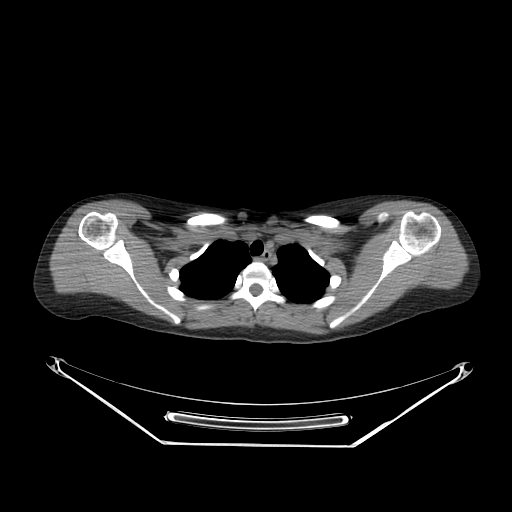
CT of an extremity soft-tissue mass (from a PET/CT study), one axial slice. Slice 213 of 267 in the series (ordered by position). 140 kVp. Soft-tissue window (W 400 / L 40 HU). 3.75 mm slice thickness. 512 × 512 image matrix, field of view 500 × 500 mm. Female patient. Case-level facts recorded for this patient, not image findings: histological type: malignant fibrous histiocytoma; grade: low; site of the primary tumour: left arm.
Annotated regions visible in this slice (expert contour drawn on MRI and transferred to this co-registered scan by the dataset authors):
- gross tumour volume (mass): box from (x=429, y=267) to (x=444, y=279) px